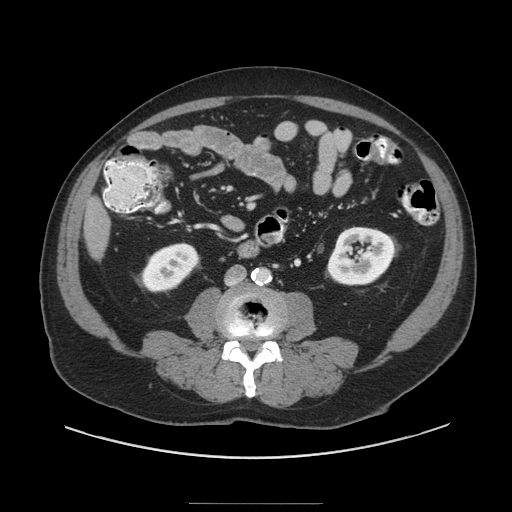
Contrast-enhanced abdominal CT (liver protocol), one axial slice; slice 16 of 91 in the series (ordered by position); 140 kVp; soft-tissue window (W 400 / L 40 HU); 2.5 mm slice thickness; 512 × 512 image matrix. Case-level facts recorded for this patient, not image findings: diagnosis: hepatocellular carcinoma (patient treated with transarterial chemoembolisation; whether this scan precedes or follows treatment is not stated here); TNM stage (as recorded): Stage-I; Child-Pugh class: A; tumour differentiation: well differentiated; tumour nodularity: uninodular.
Outlined on this slice (semi-automatically segmented with operator editing):
- liver parenchyma outside the tumour (the mass and vessels are separate outlines, so this box may not span the whole liver): bounding box (x1, y1, x2, y2) in pixels: (84, 198, 110, 258)